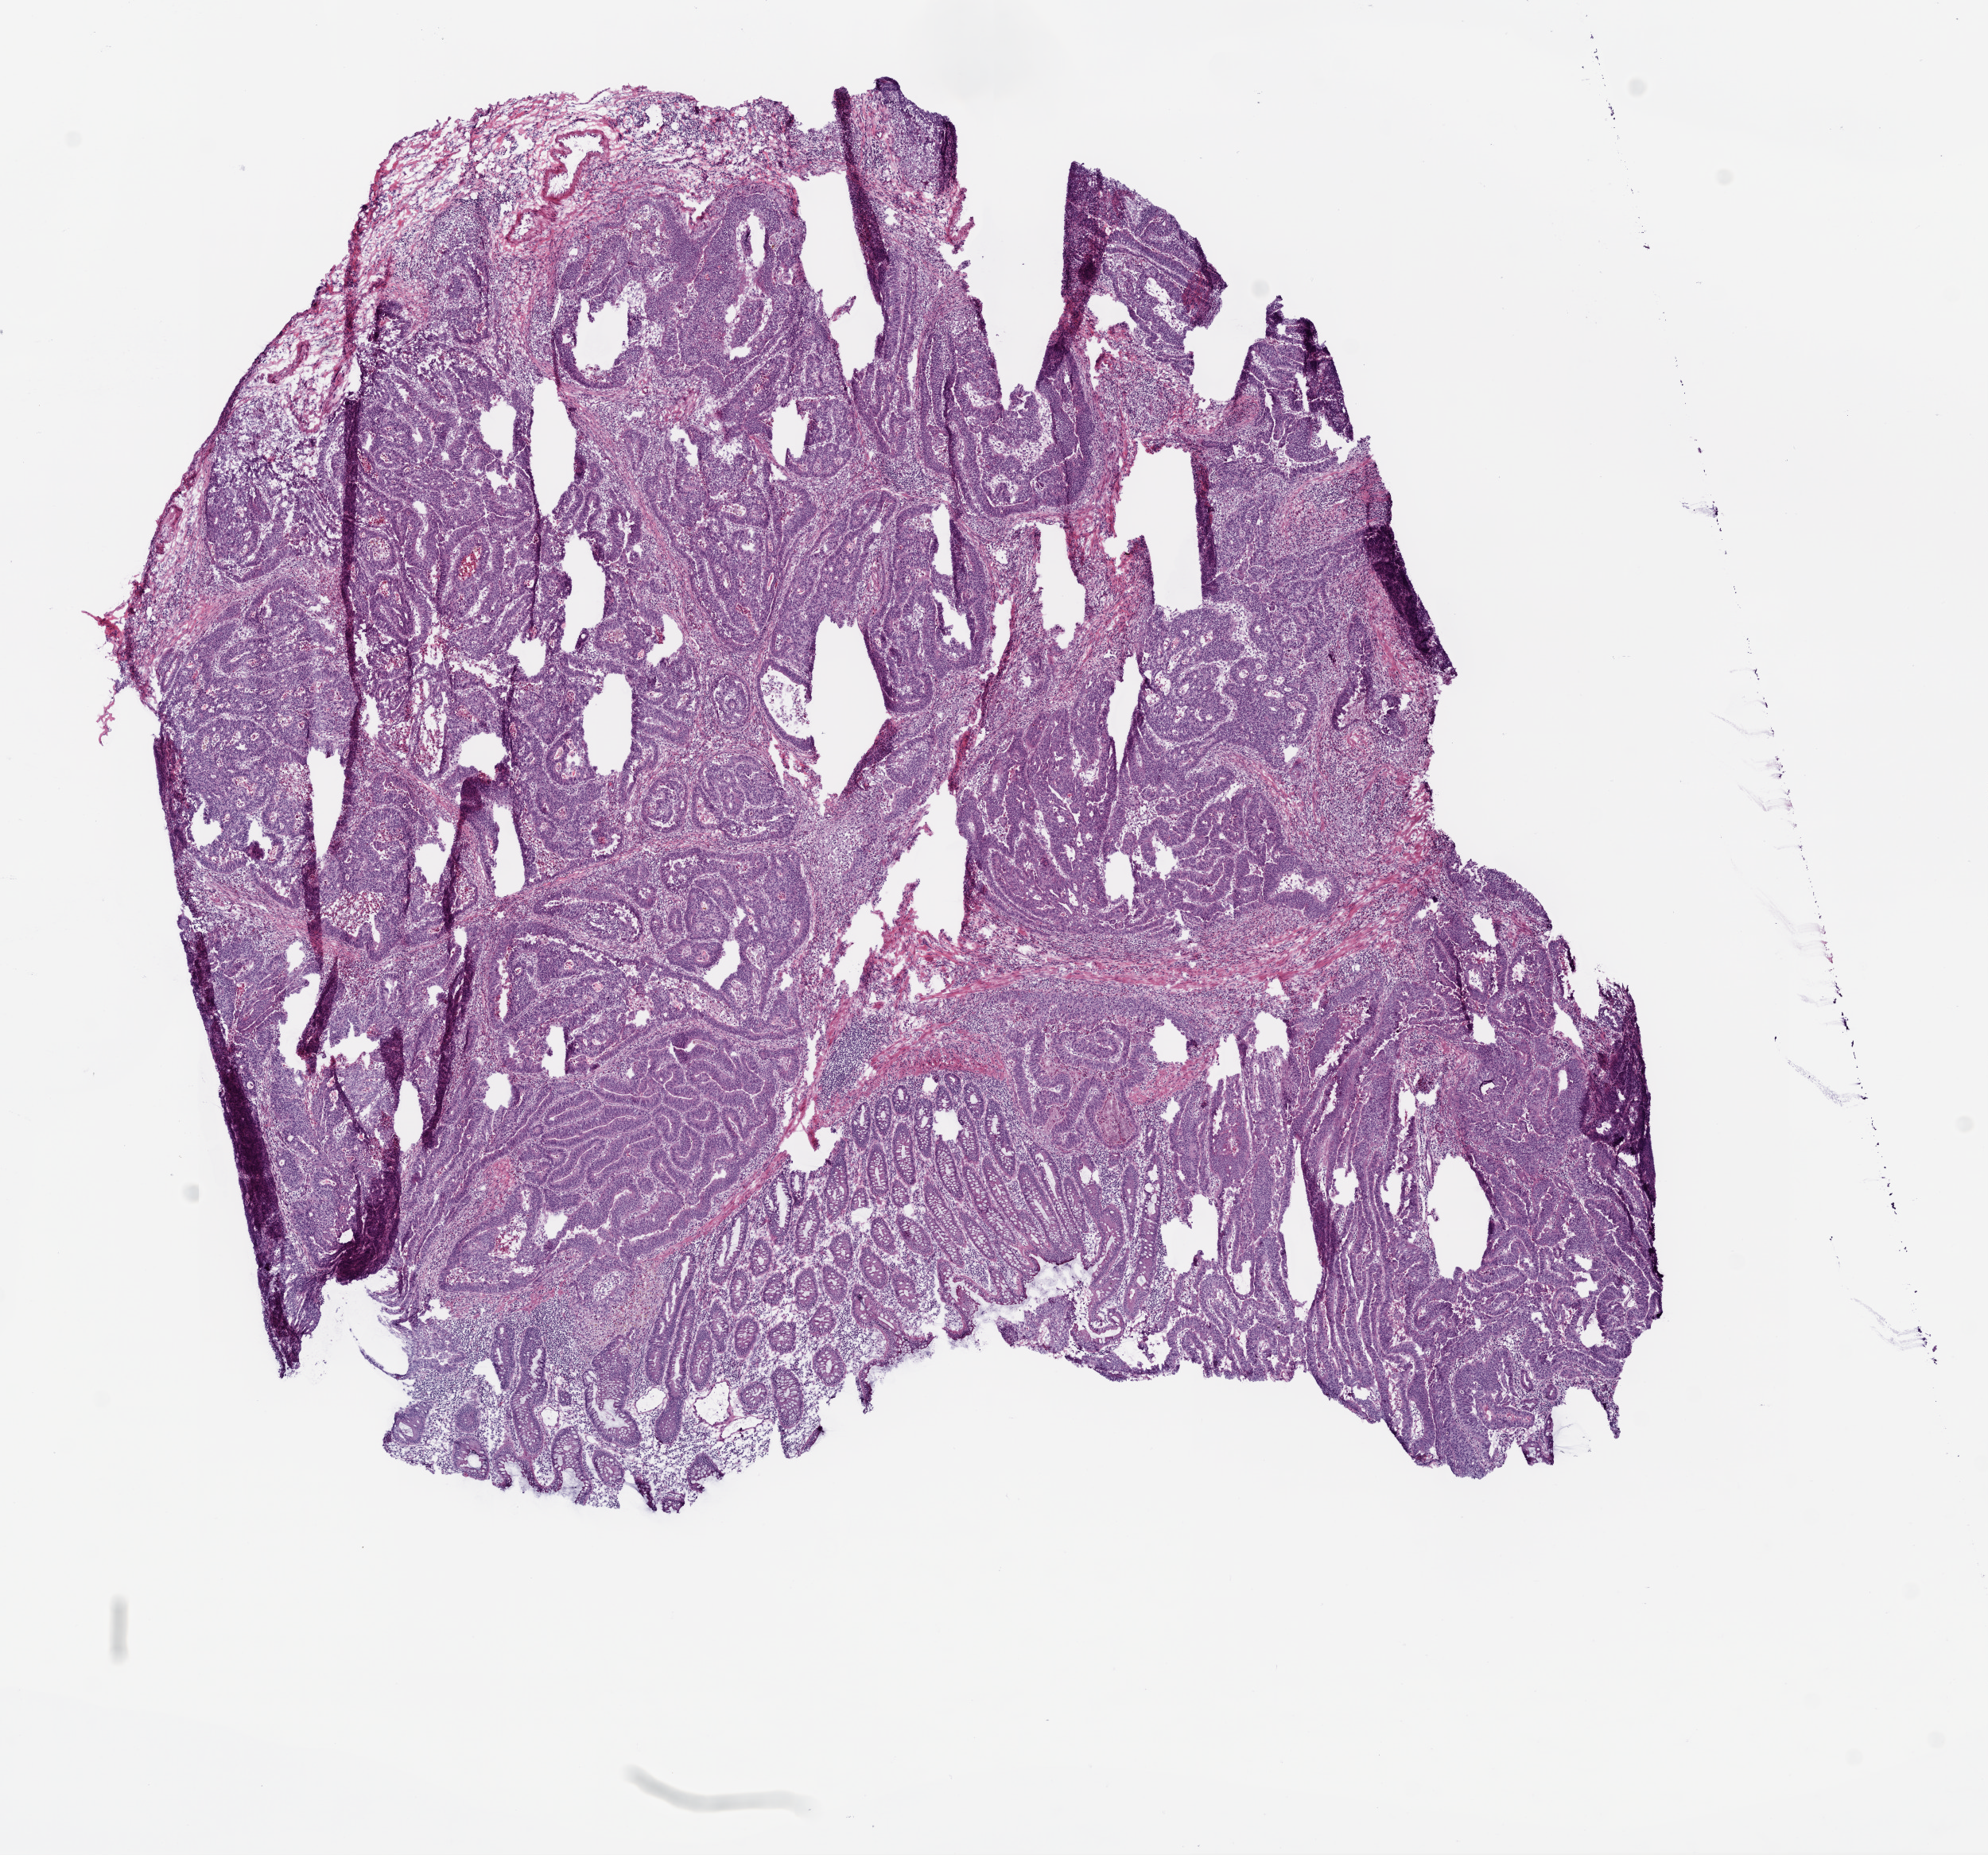
H&E-stained whole-slide image, low-resolution overview of the scanned area, about 10.0 x 9.4 mm. Frozen section from the top of the tissue portion. Sample: primary tumour, rectum. Male patient; age at initial diagnosis 61 years.
Pathologic diagnosis: Adenocarcinoma, NOS (rectosigmoid junction).